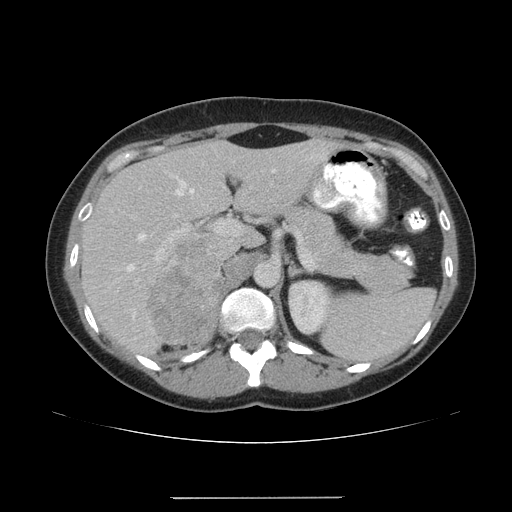
Contrast-enhanced abdominal CT, one axial slice; slice 114 of 161 in the series (ordered by position); reconstruction kernel STANDARD; intravenous contrast given; soft-tissue window (W 400 / L 40 HU); 512 × 512 image matrix. Female patient. From the clinical record (not read from this slice): diagnosis: adrenocortical carcinoma; tumour side: right adrenal; tumour size at pathology: 9 cm; Ki-67 index: 14 %; stage (as recorded): 3.
Outlined on this slice (semi-automatic segmentation, software-assisted and operator-edited):
- mass: box from (x=151, y=246) to (x=222, y=341) px